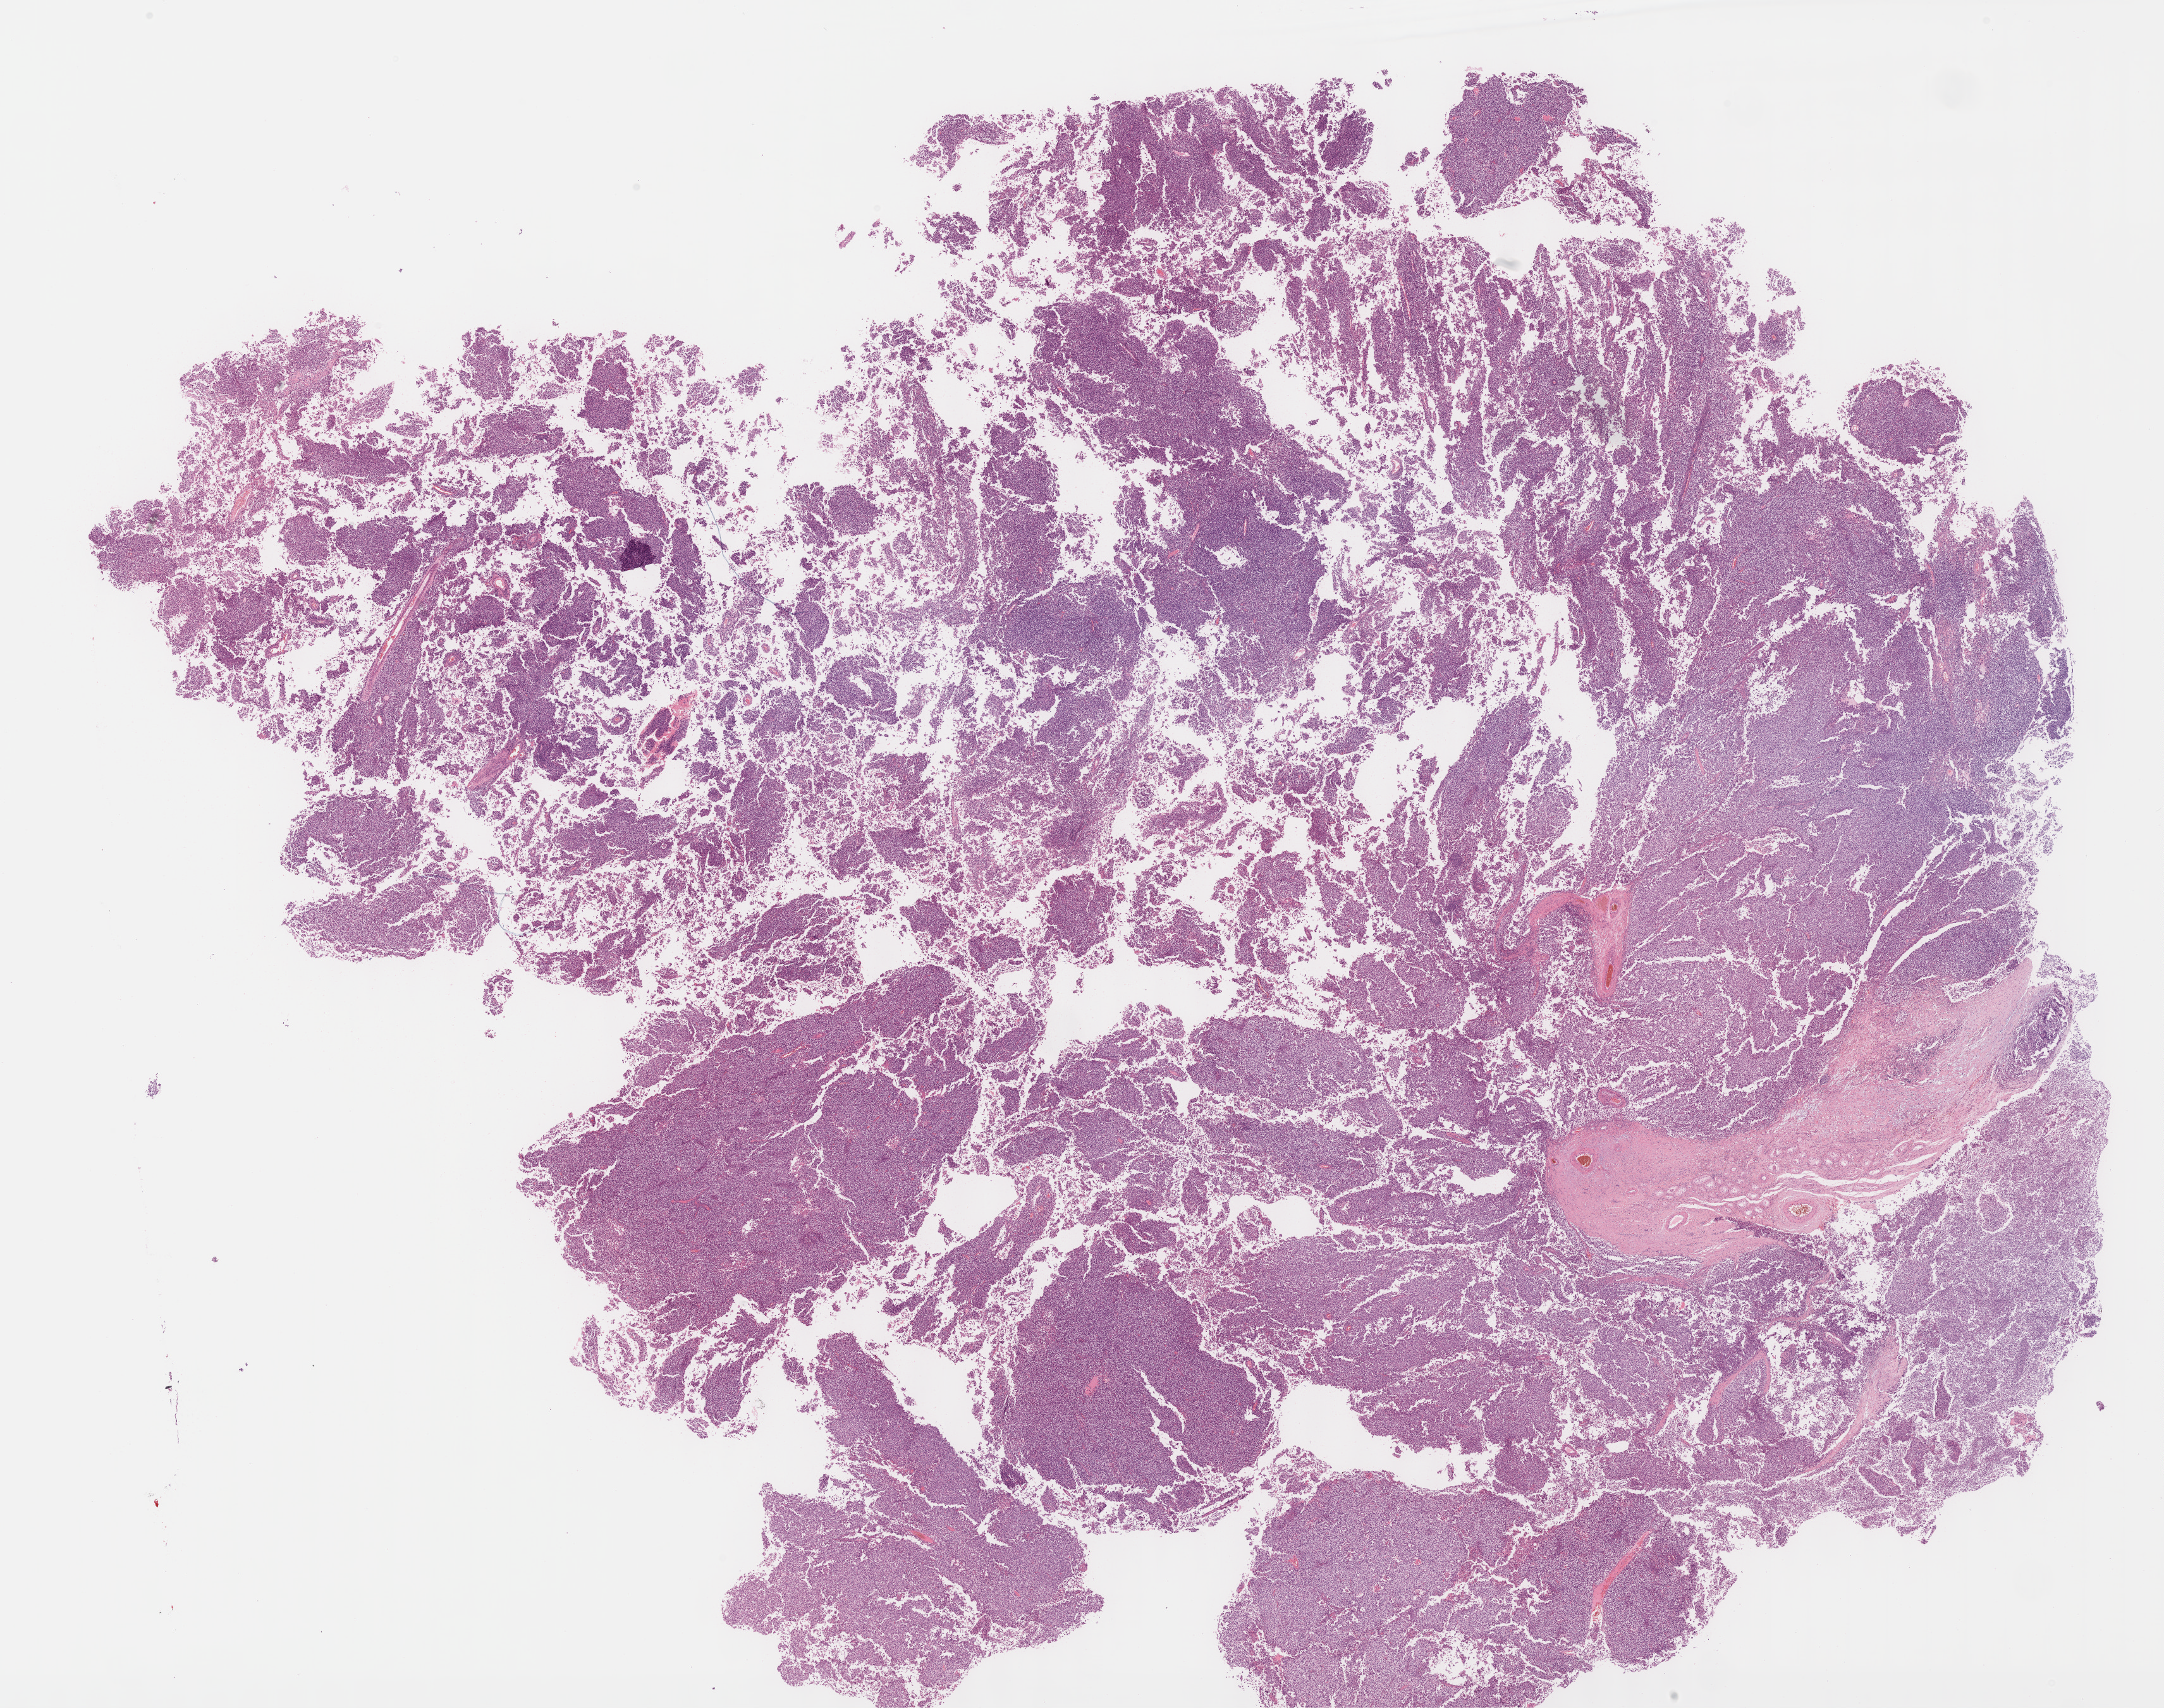
Digitized Hematoxylin and eosin (H&E) stained tissue section (whole slide), a low-resolution overview of the entire scanned area, about 27.7 x 21.8 mm (acquisition: 40x scan). Formalin-fixed paraffin-embedded (FFPE) diagnostic section. Primary tumour sample from the testis. Male, age 33 years at initial diagnosis.
- AJCC pathologic stage: I (6th edition)
- histologic diagnosis: Seminoma, NOS
- laterality: right